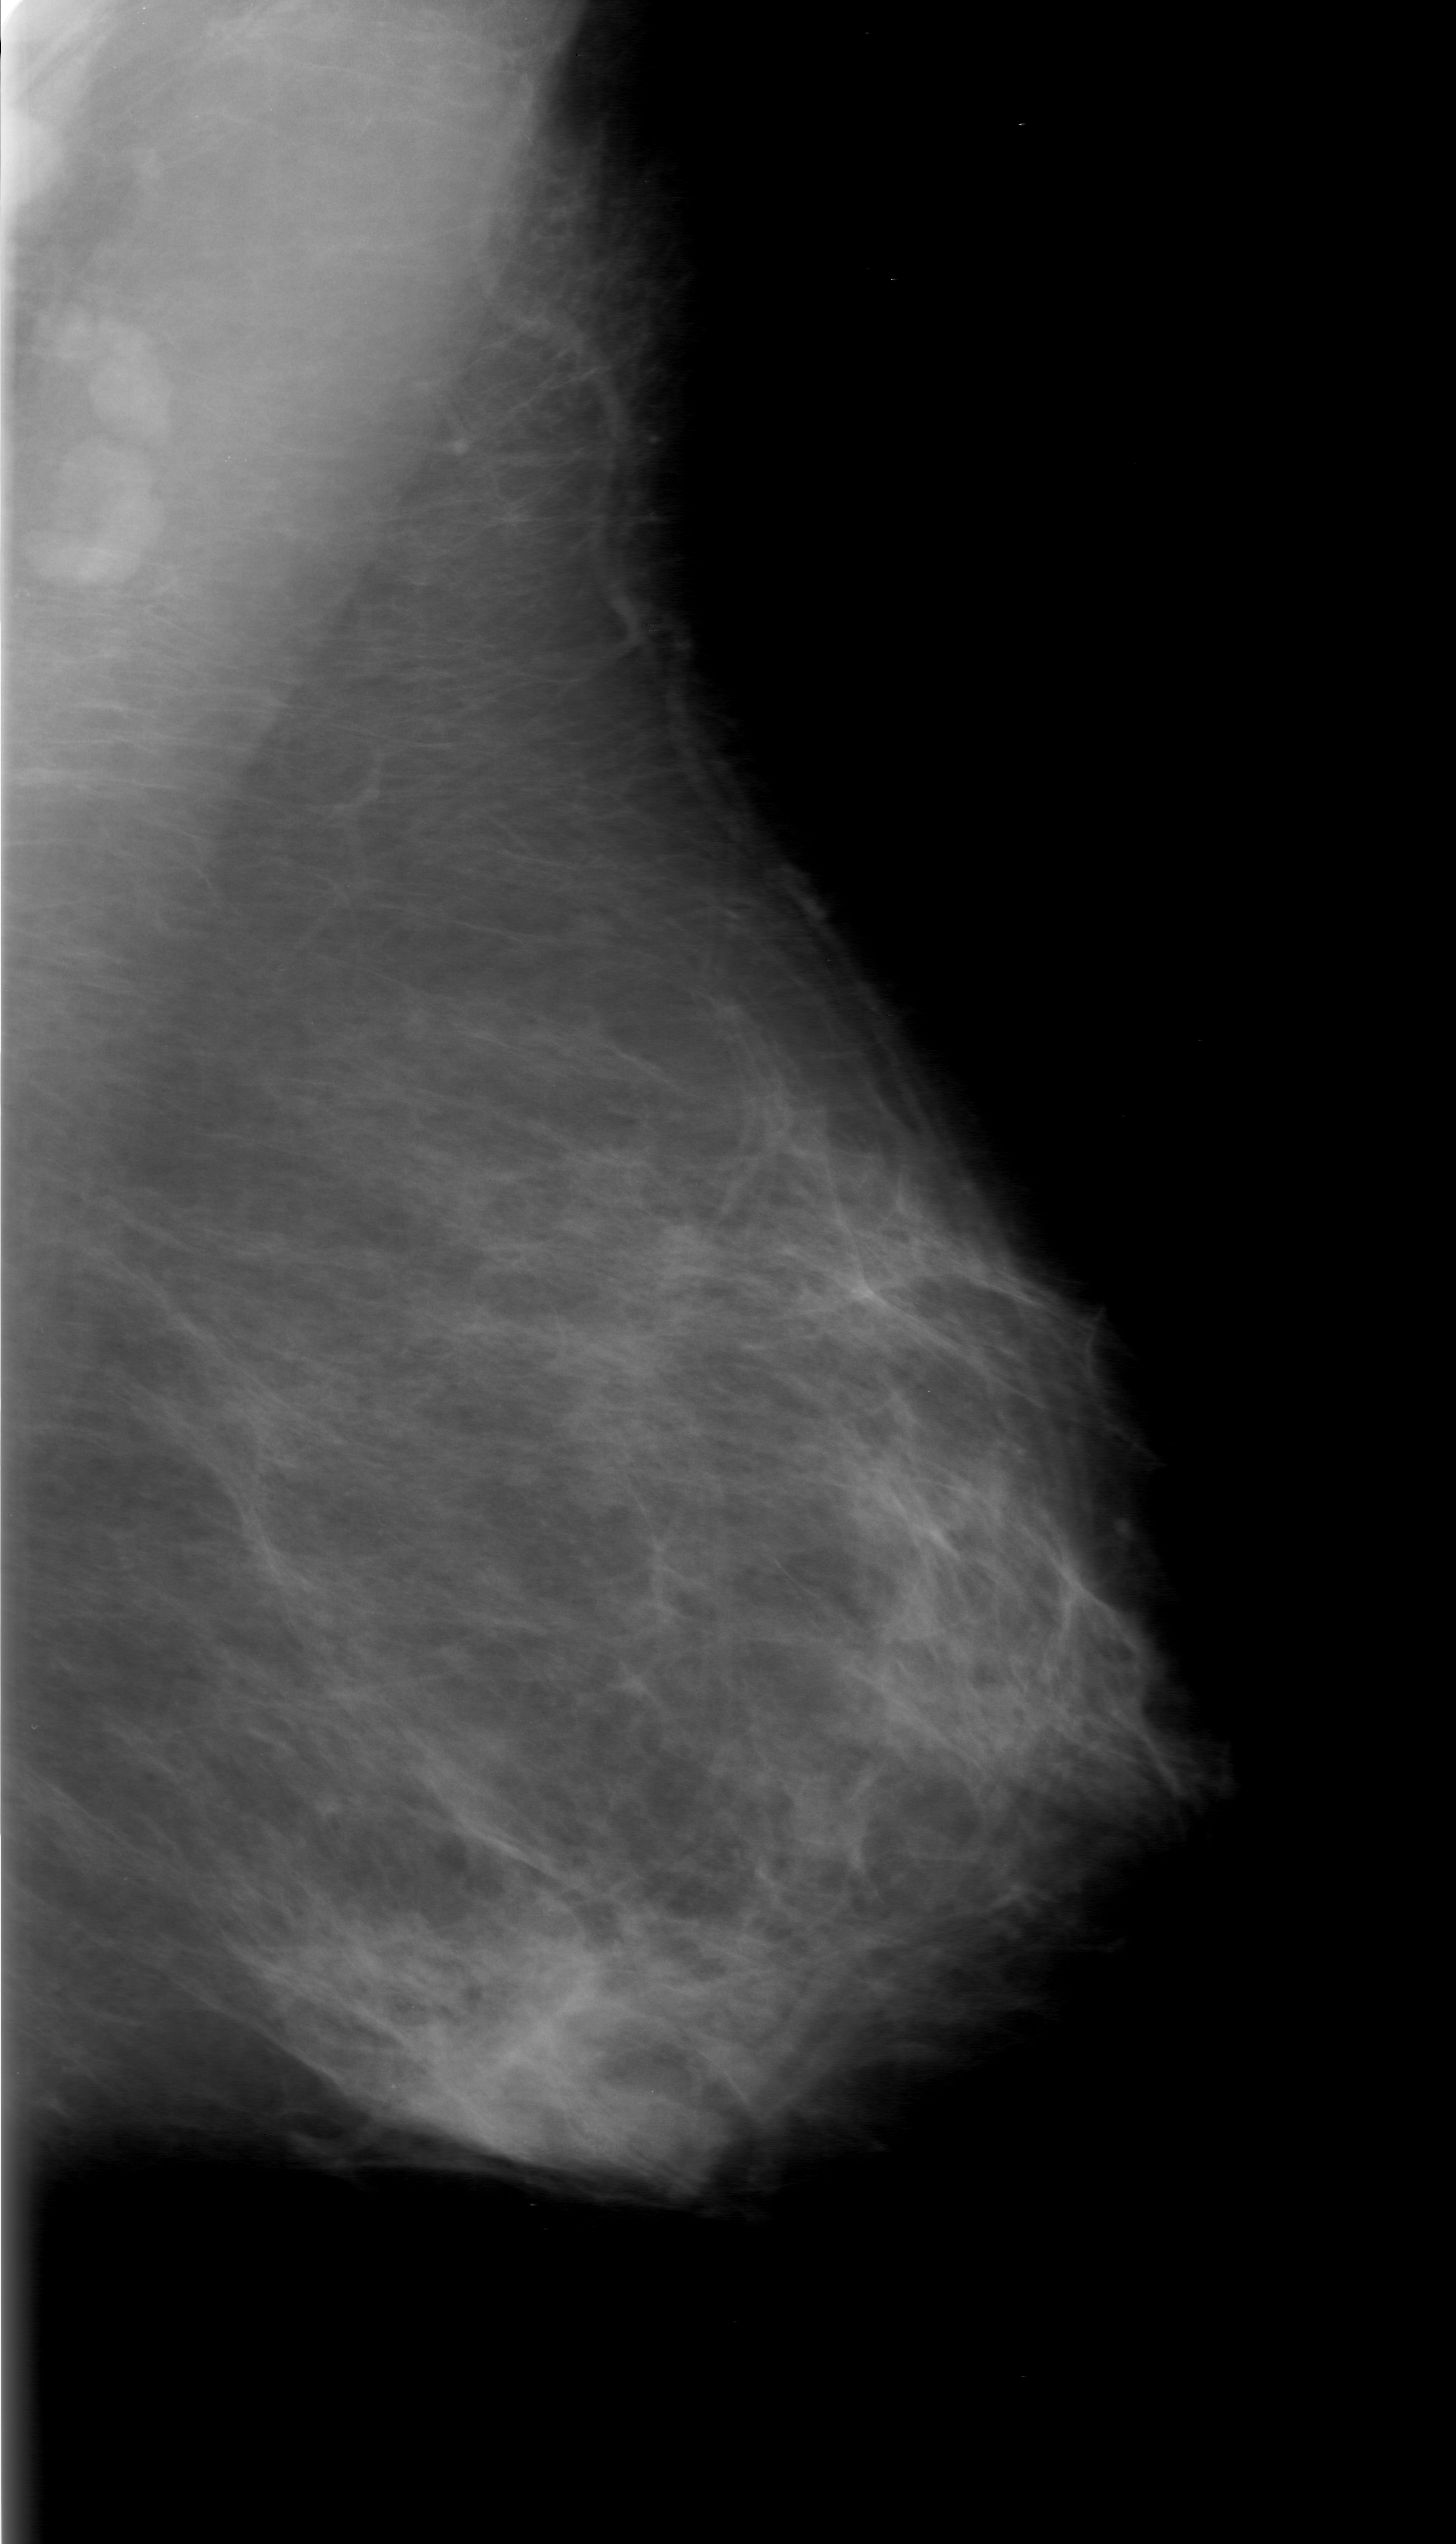
Digitized screen-film mammogram; left breast; MLO view; breast composition: scattered fibroglandular densities (BI-RADS density category 2 of 4).
Marked findings (only marked abnormalities are described; nothing is implied about the rest of the image): calcifications, morphology amorphous, distribution clustered; BI-RADS assessment category 0 (incomplete: needs additional imaging); pathology result (as recorded, not read from the image): malignant.